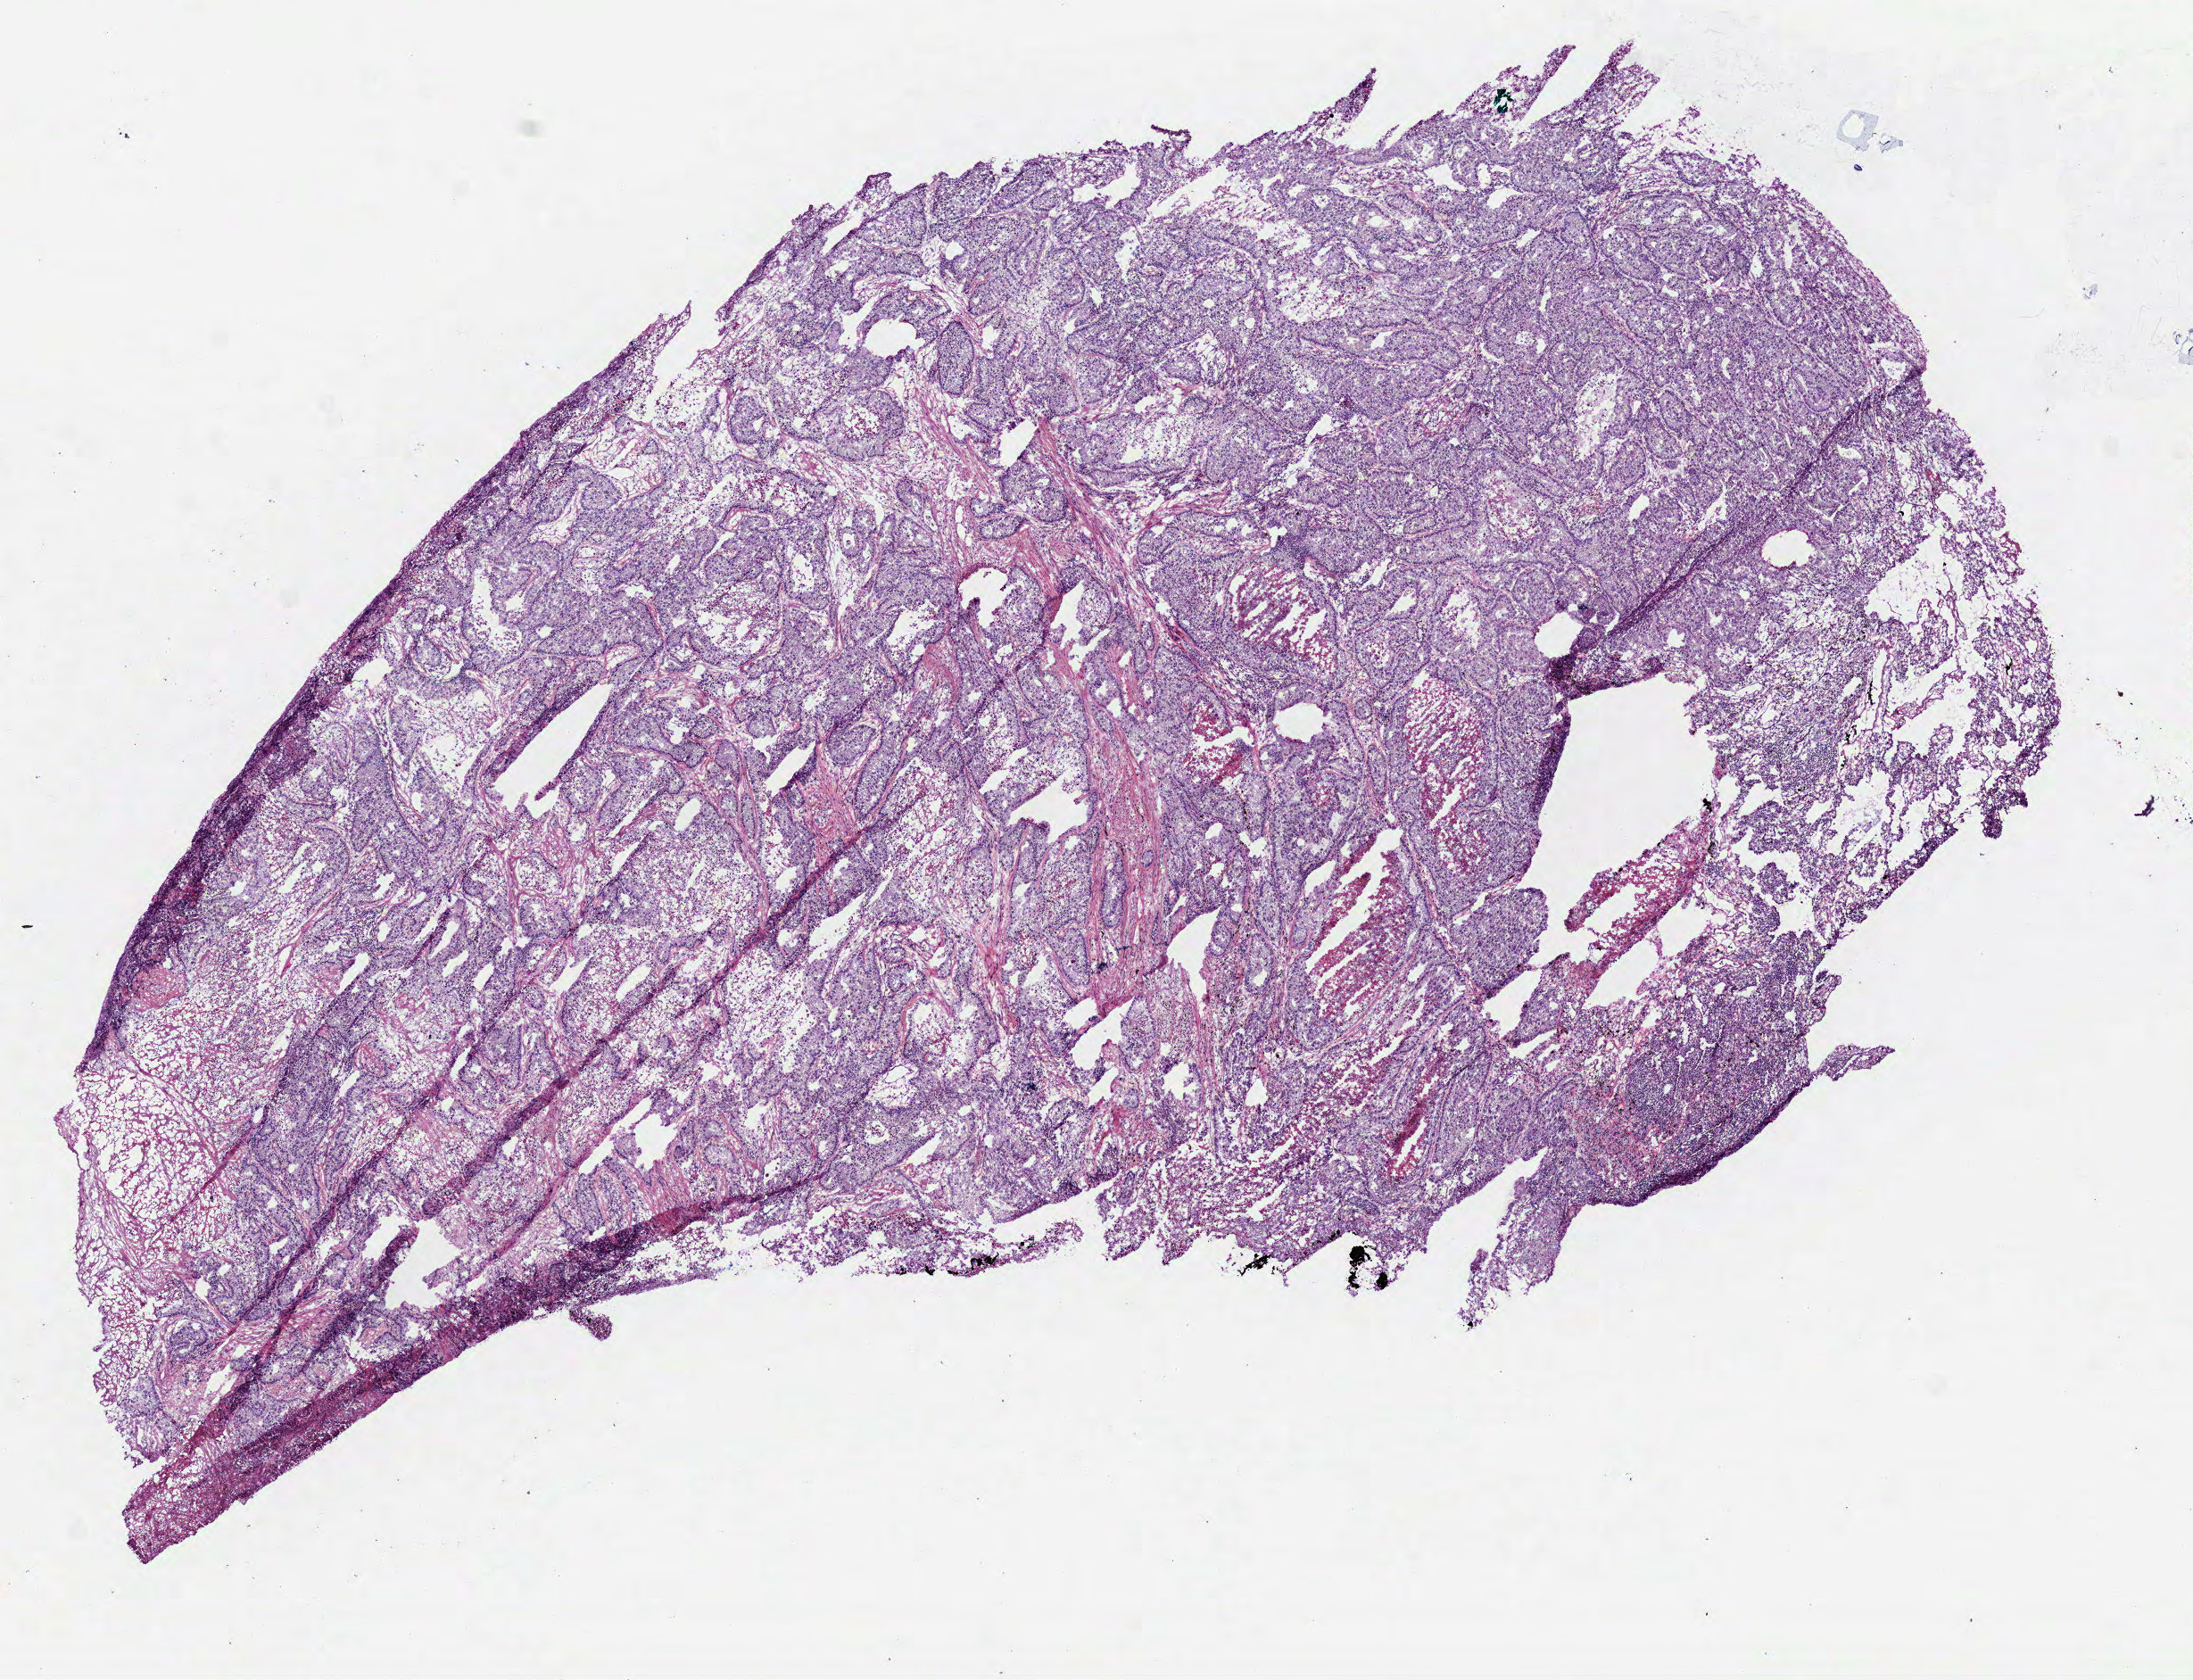
Hematoxylin and eosin (H&E) stained whole-slide image, a low-resolution overview of the entire scanned area, about 9.9 x 7.6 mm, frozen section, primary tumour sample from the lung. Patient: female, age at initial diagnosis 50 years. Pathologist review of this section (percent, as recorded): tumour cells 75%, tumour nuclei 75%, normal cells 0%, stromal cells 15%, necrosis 10%.
AJCC pathologic stage: IIA. Pathologic diagnosis: Adenocarcinoma, NOS (lower lobe, lung).